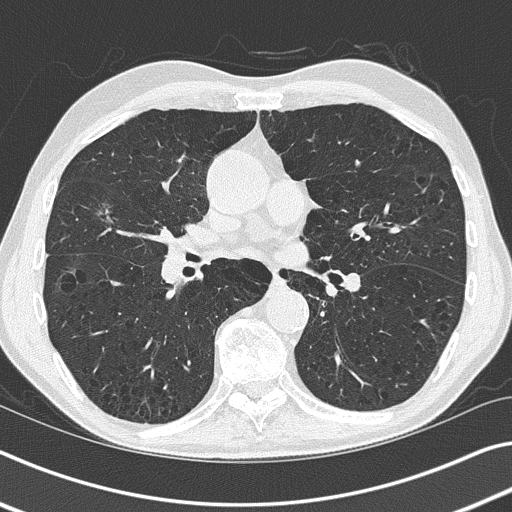
Axial slice from a low-dose chest CT screening exam, baseline screening round, lung window (W 1500 / L -600 HU), lung (sharp) reconstruction kernel (B50f), 120 kVp, slice 79 of 155 in the series, 512 × 512 image matrix, field of view 340 × 340 mm. Male, age 73 years at enrolment.
Expert-annotated lung lesion, bounding box [x1, y1, x2, y2] px = [82, 189, 132, 235]. The screening reader recorded 3 non-calcified nodules or masses ≥4 mm on this exam (right upper lobe, right middle lobe, right upper lobe); which of them this box marks is not recorded. Official screen result: positive, change unspecified: nodule(s) >= 4 mm or enlarging nodule(s), mass(es), or other non-specific abnormalities suspicious for lung cancer. Lung cancer was diagnosed 45 days after this screen: bronchiolo-alveolar adenocarcinoma, NOS, right middle lobe, well differentiated (G1), stage IA (AJCC 6th edition), 11 mm at pathology.